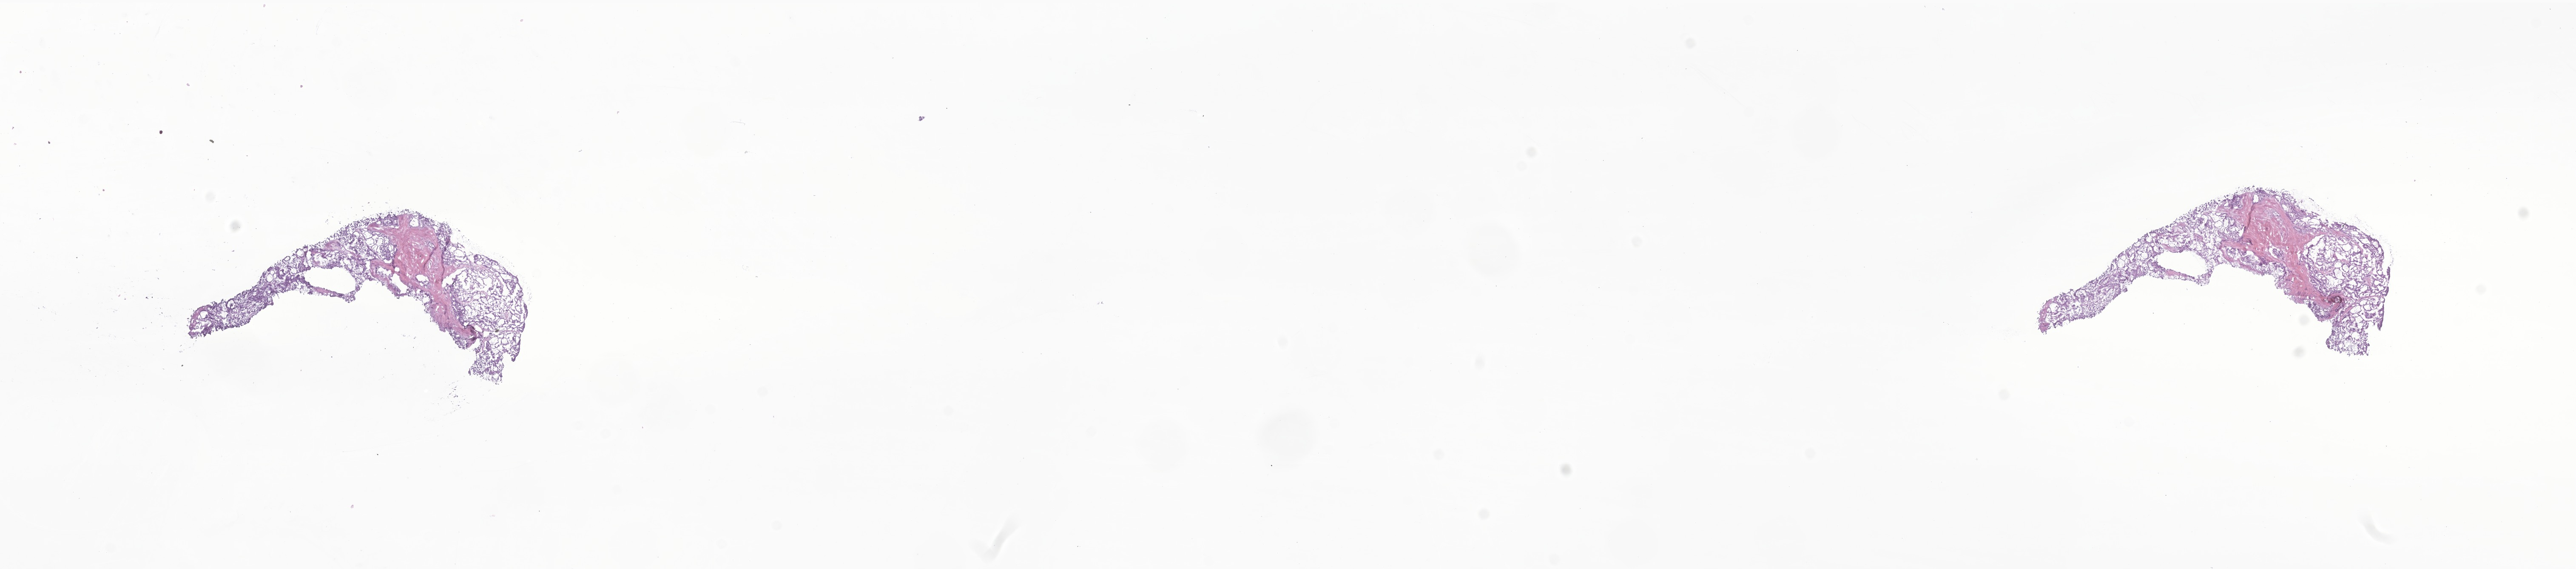
Whole-slide image, hematoxylin and eosin (H&E) stain of tumor tissue from the thyroid — low-resolution overview of the scanned area, about 25.5 x 5.6 mm; cryosection (OCT / tissue freezing medium). Patient female; age 161 months.
- diagnosis (ICD-O-3 morphology term): Papillary carcinoma, NOS